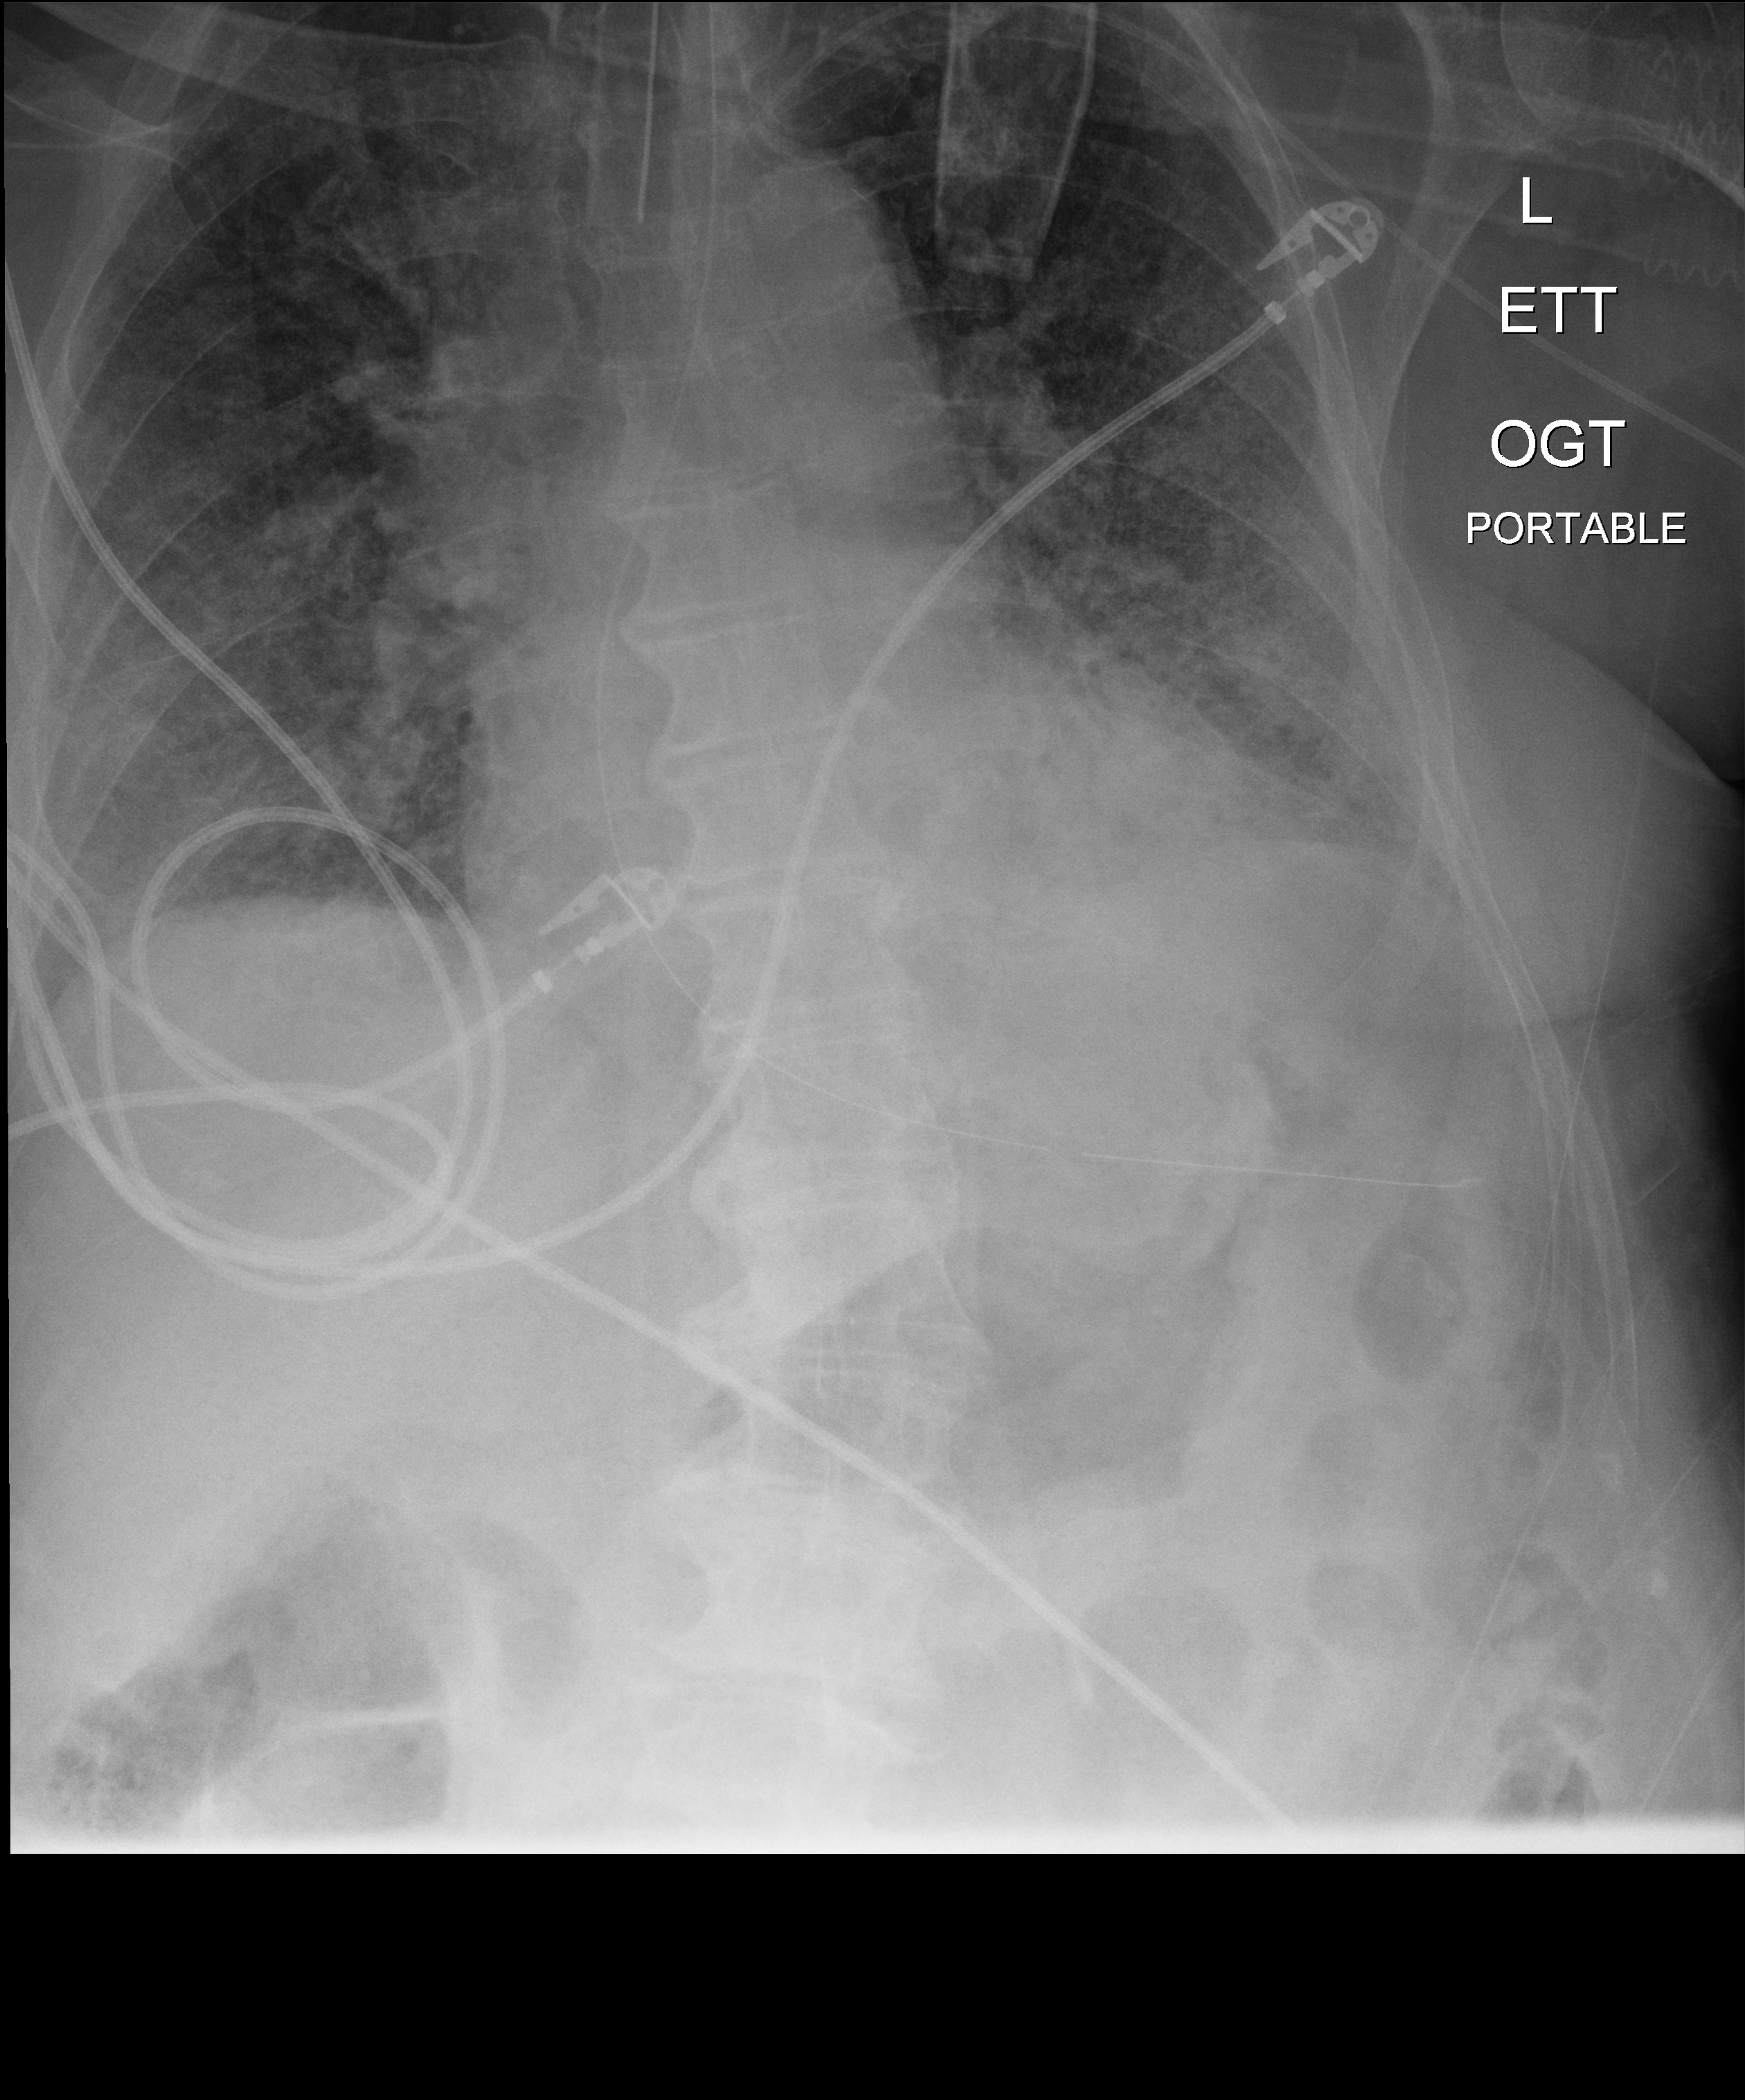
Portable chest radiograph, anteroposterior (AP) projection. Patient hospitalised with COVID-19; male, aged 75–90 years.
From the hospital-stay record, not from the radiograph (when in the stay this image was taken is not recorded): diabetes (admission record): no; admitted to intensive care during this hospital stay: yes.